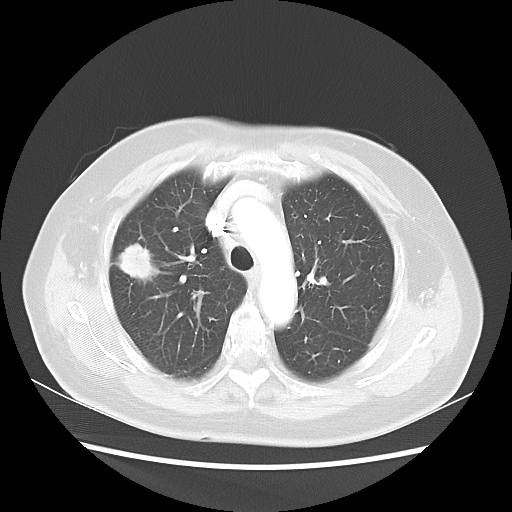
Chest CT, one axial slice. Lung window (W 1500 / L -600 HU). 5 mm slice thickness. 512 × 512 image matrix, field of view 360 × 360 mm. Patient: female, 75 years. Case-level facts recorded for this patient, not image findings: clinical TNM (as recorded): T1c N0 M0.
Outlined on this slice (bounding box drawn by a radiologist):
- lung tumour (recorded histology: adenocarcinoma): bounding box [x1, y1, x2, y2] px = [112, 238, 157, 292]